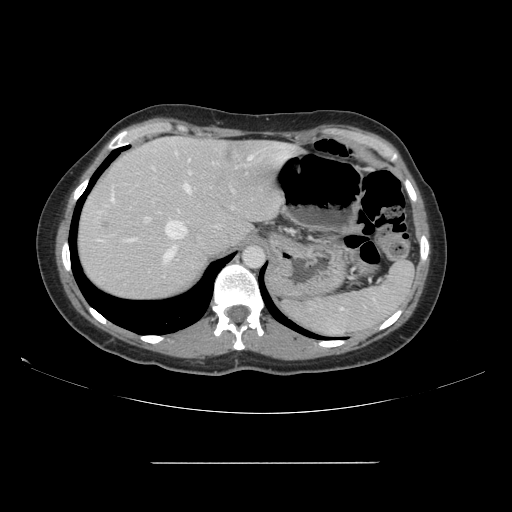
Contrast-enhanced abdominal CT, one axial slice; slice 119 of 151 in the series (ordered by position); 120 kVp; intravenous contrast given; soft-tissue window (W 400 / L 40 HU); 2.5 mm slice thickness; 512 × 512 image matrix, field of view 421 × 421 mm. Female patient, age 46 years. From the clinical record (not read from this slice): diagnosis: colorectal cancer liver metastases, imaged before liver resection; multiple liver metastases: yes; largest metastasis: 3 cm; chemotherapy before resection: no.
Structures marked on this image (outlined manually by an expert reader):
- hepatic veins: box from (x=111, y=153) to (x=257, y=242) px
- liver: (x=78, y=137)–(x=297, y=301)
- planned liver remnant (the part of the liver to remain after resection): (x=91, y=137)–(x=294, y=250)
- portal vein (with intrahepatic branches): (x=163, y=172)–(x=190, y=264)
- liver metastasis: (x=224, y=147)–(x=235, y=163)